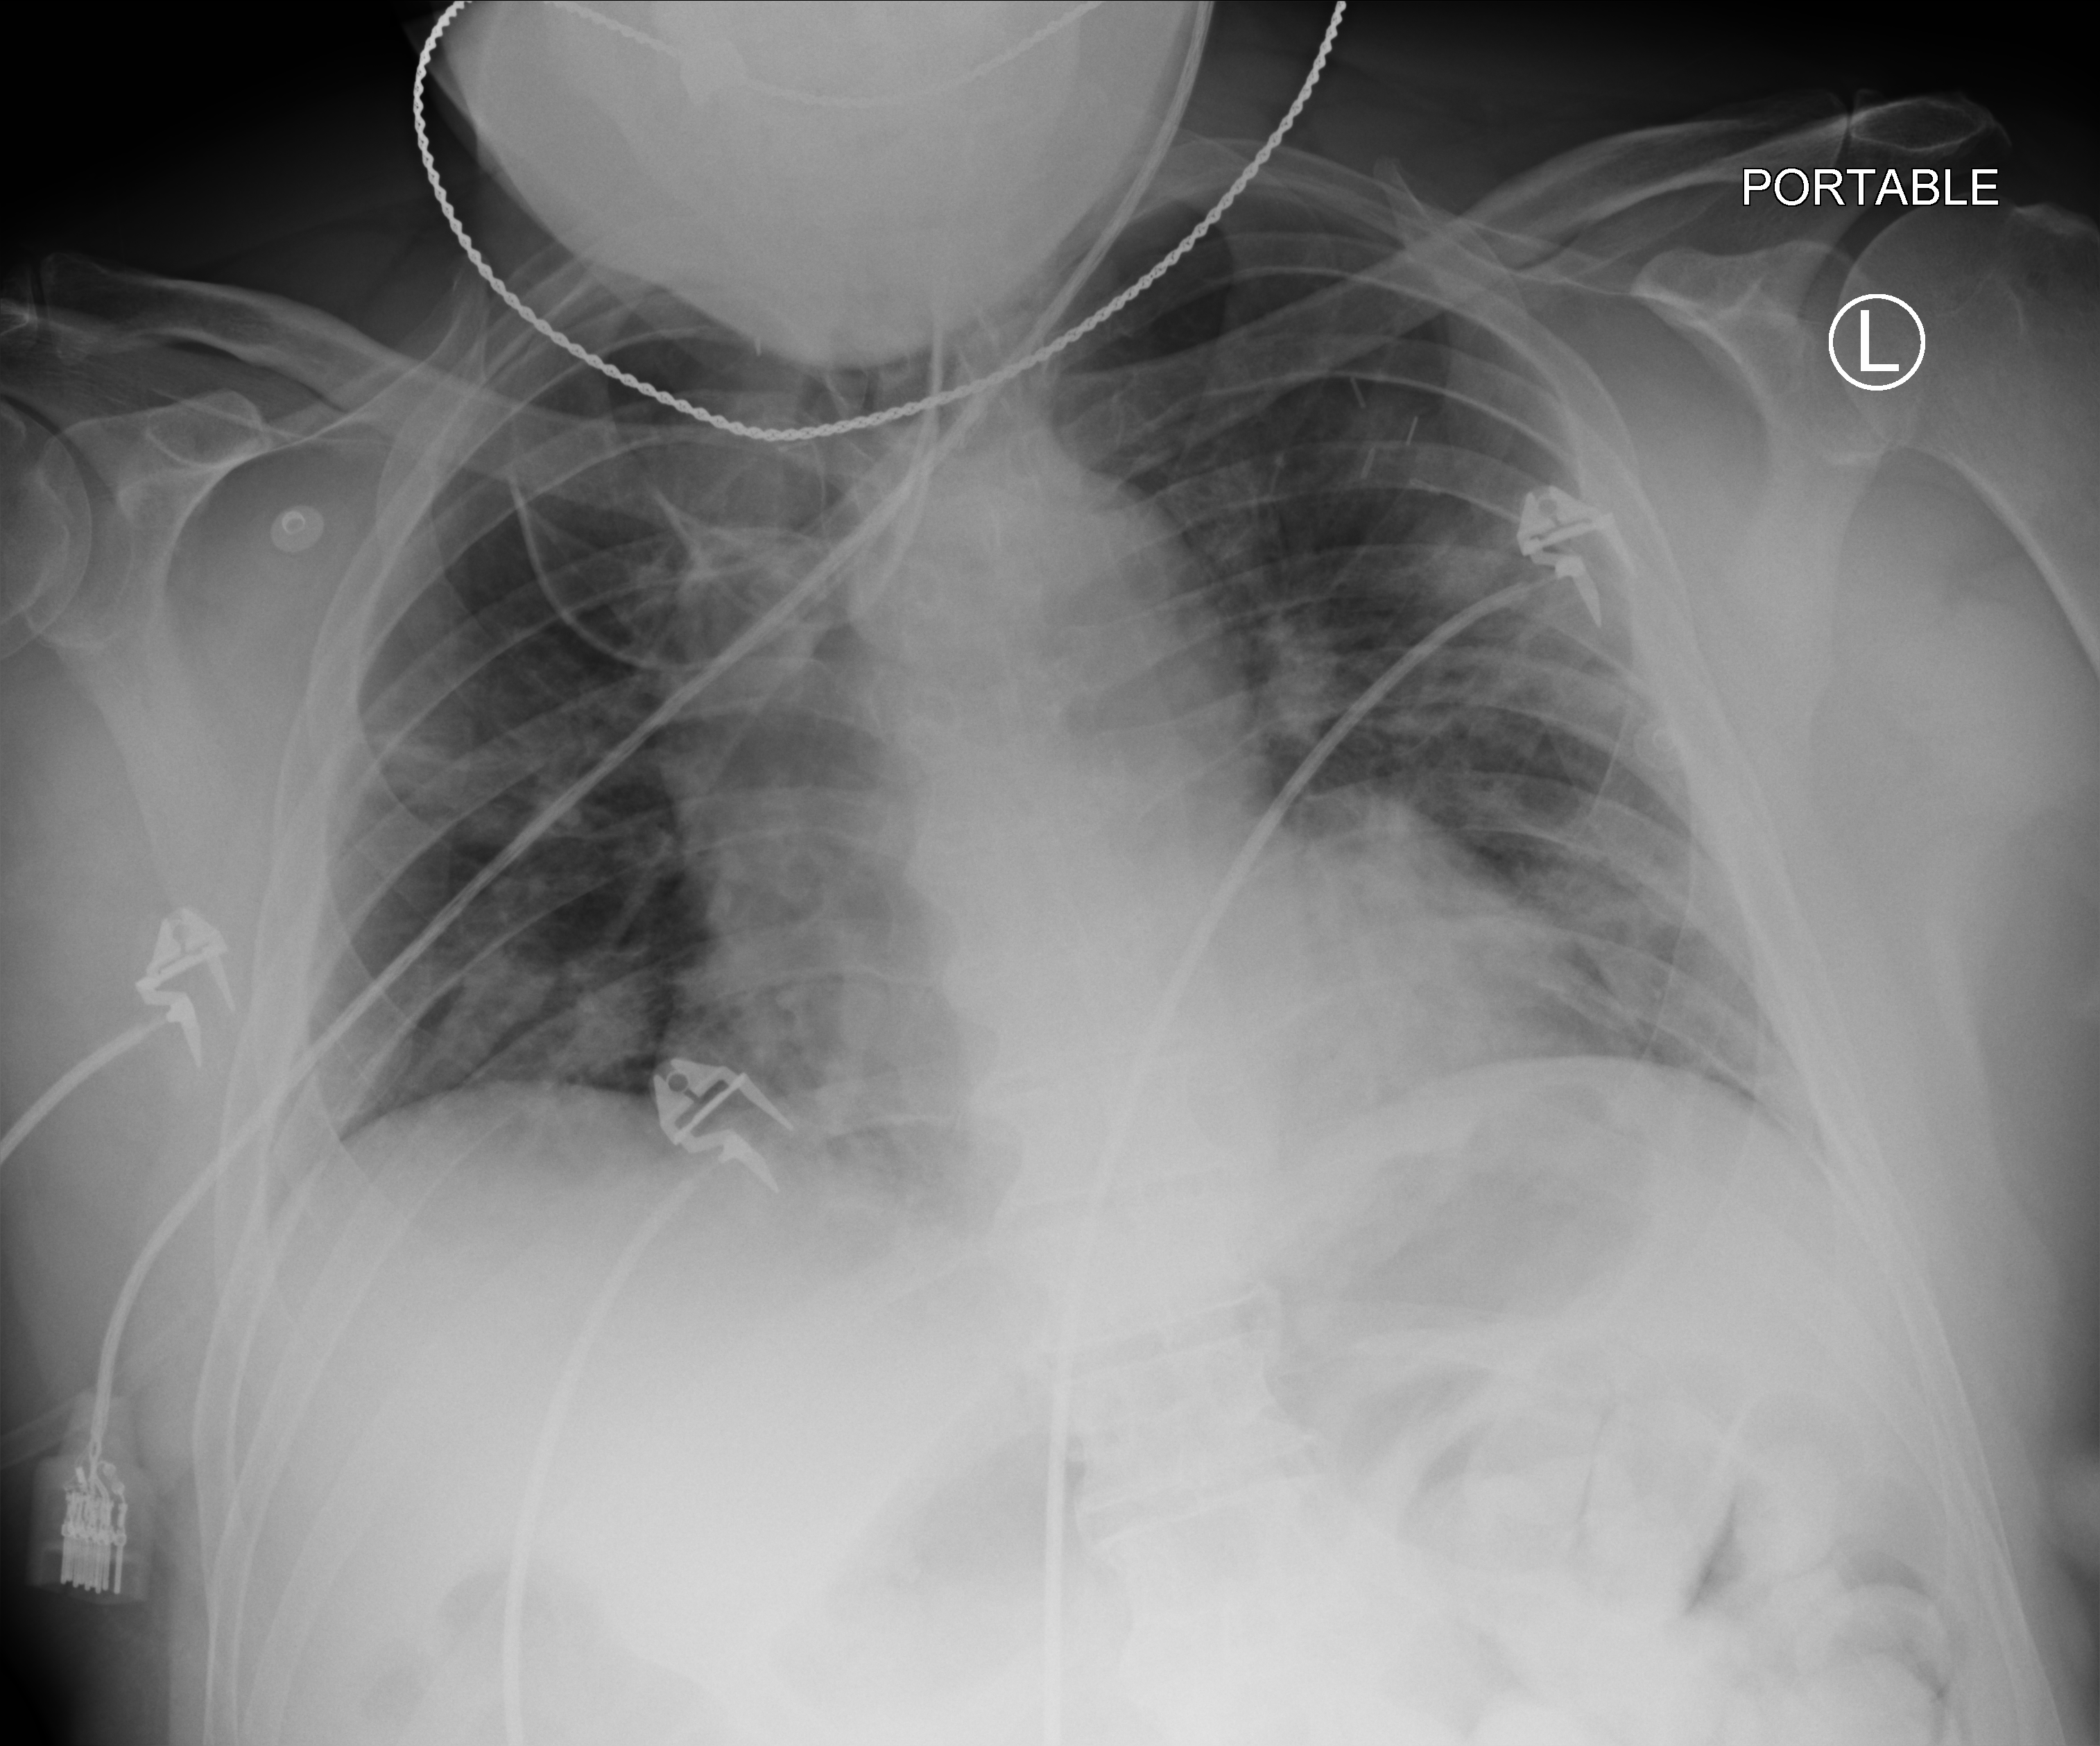
Bedside chest radiograph (computed radiography), anteroposterior (AP) projection. Adult patient hospitalised with COVID-19, age 18–59 years.
Hospital-stay facts (about this admission, not read from this image; timing relative to this image not recorded): smoking status (admission record): never; COPD (admission record): no; mechanically ventilated during this hospital stay: yes.